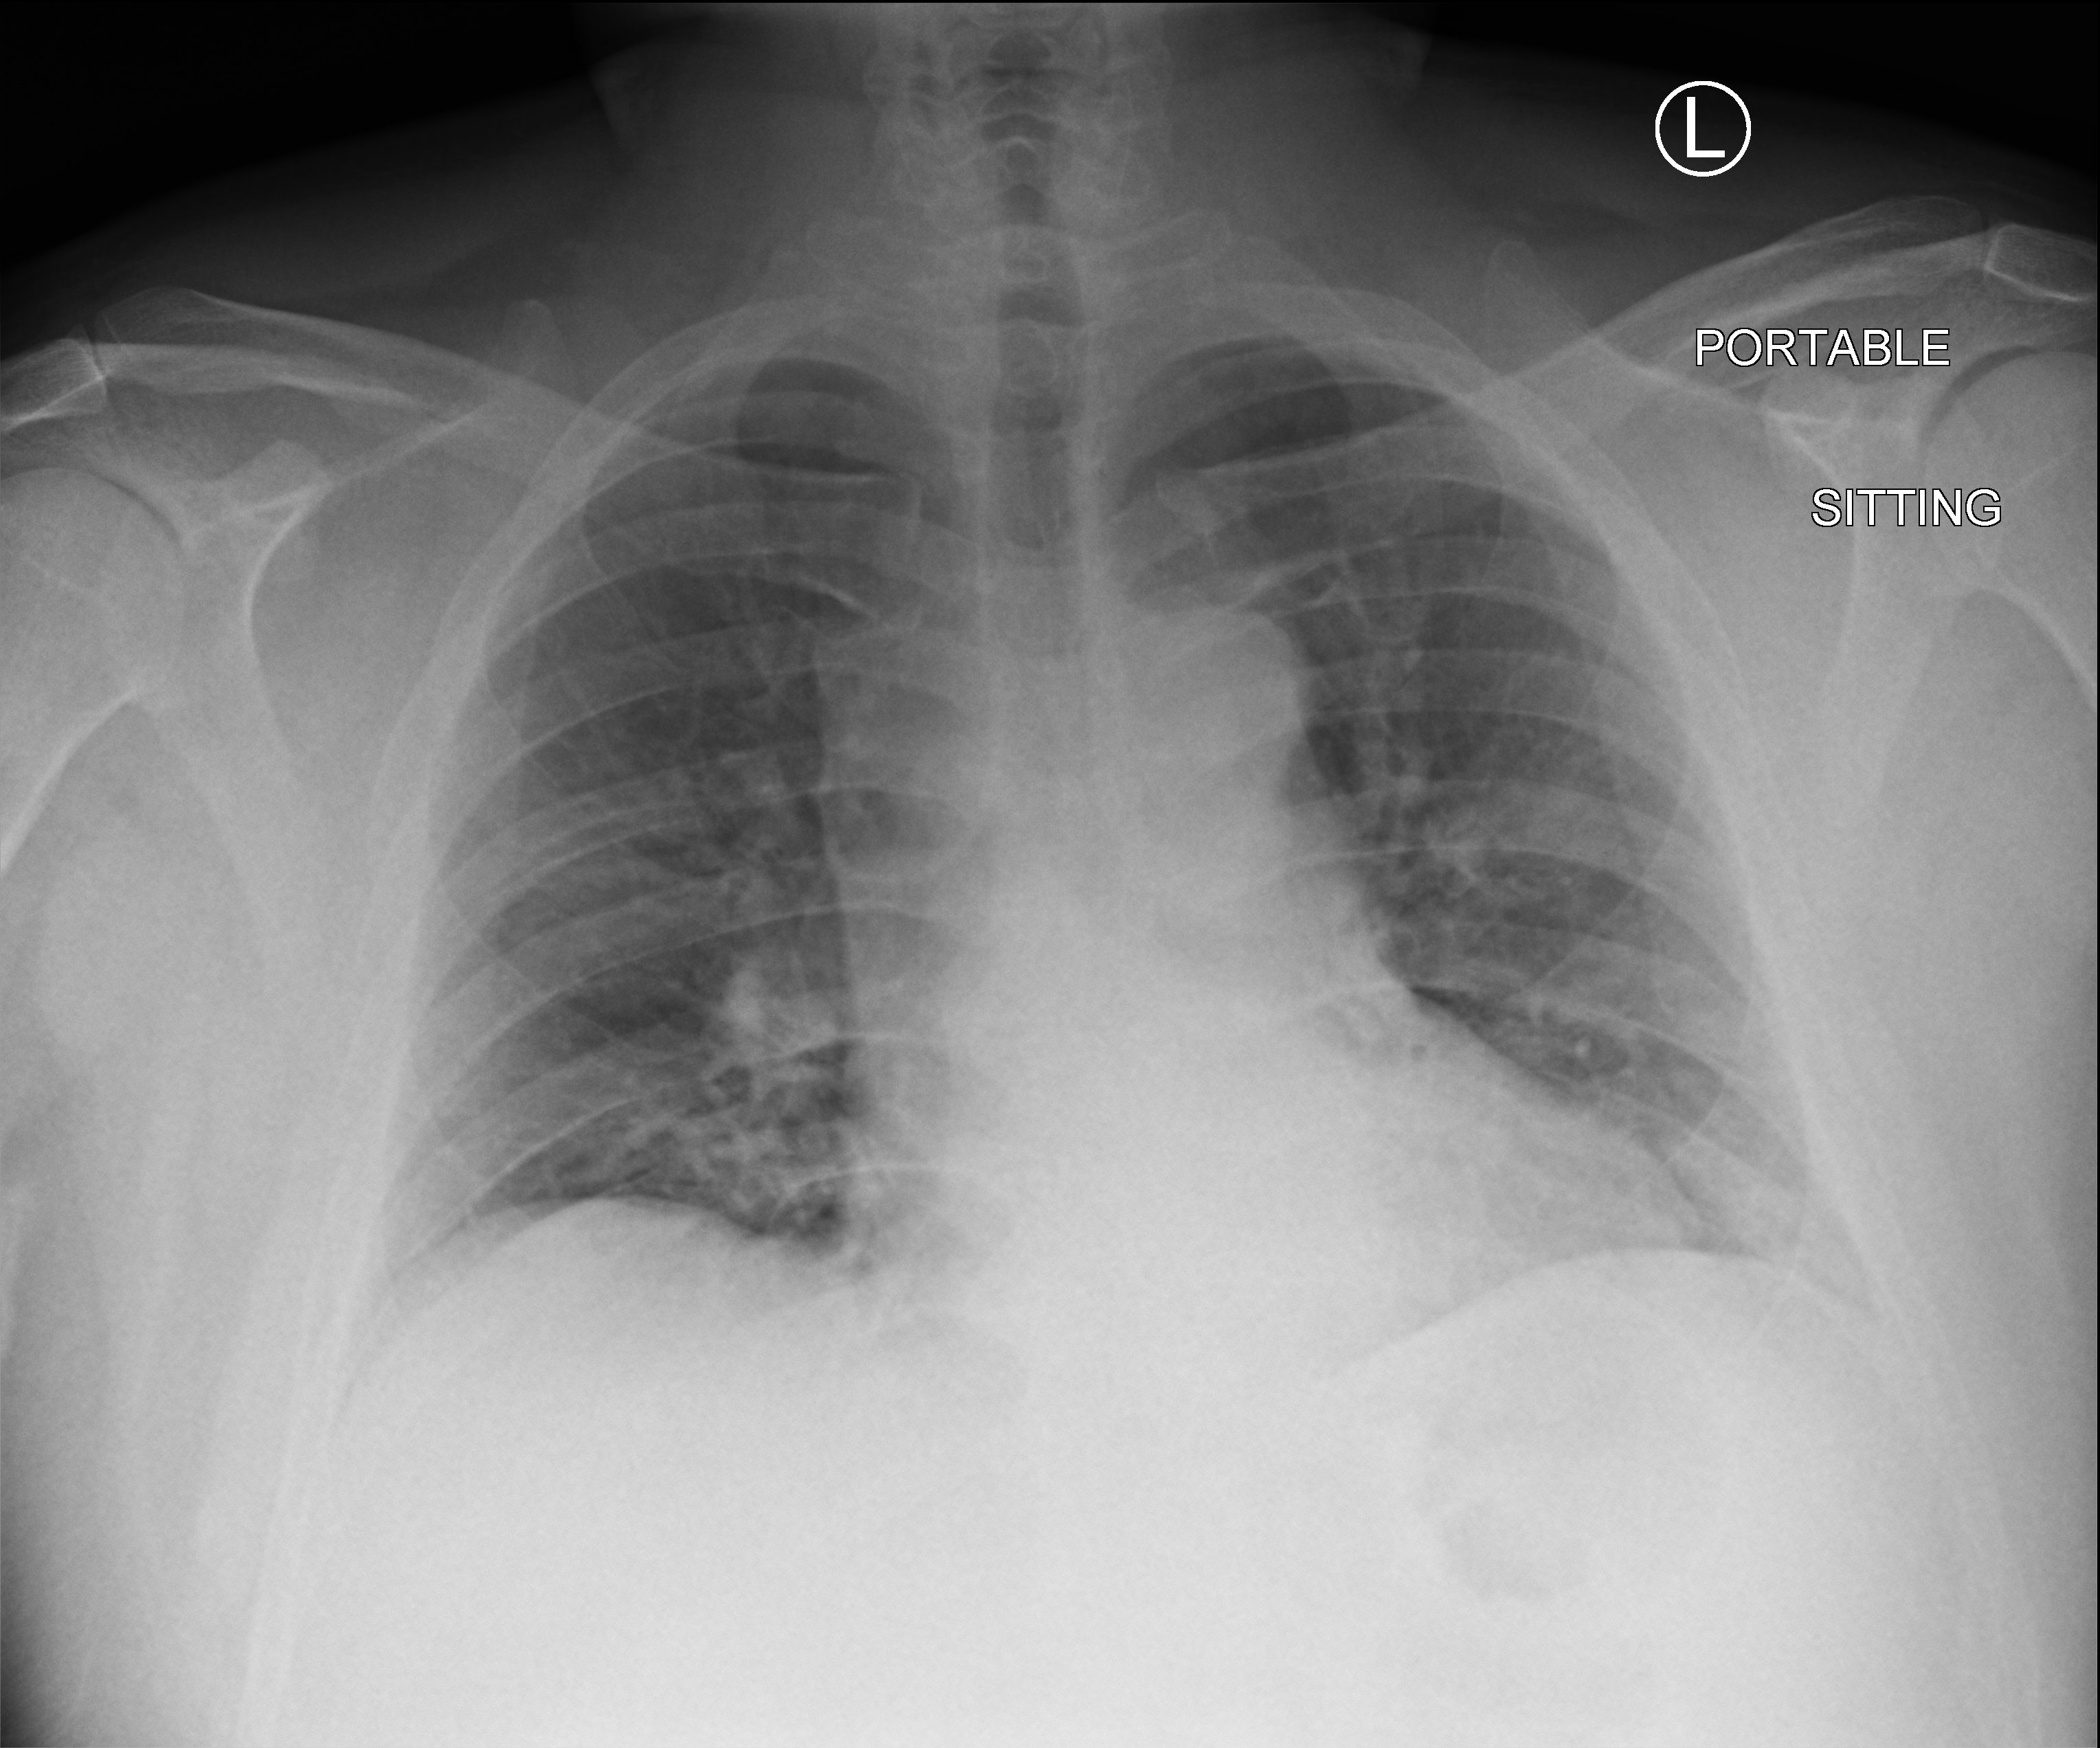
Bedside chest radiograph (computed radiography). Patient hospitalised with COVID-19; male, aged 18–59 years.
From the hospital-stay record, not from the radiograph (when in the stay this image was taken is not recorded): mechanically ventilated during this hospital stay: no; admitted to intensive care during this hospital stay: no.